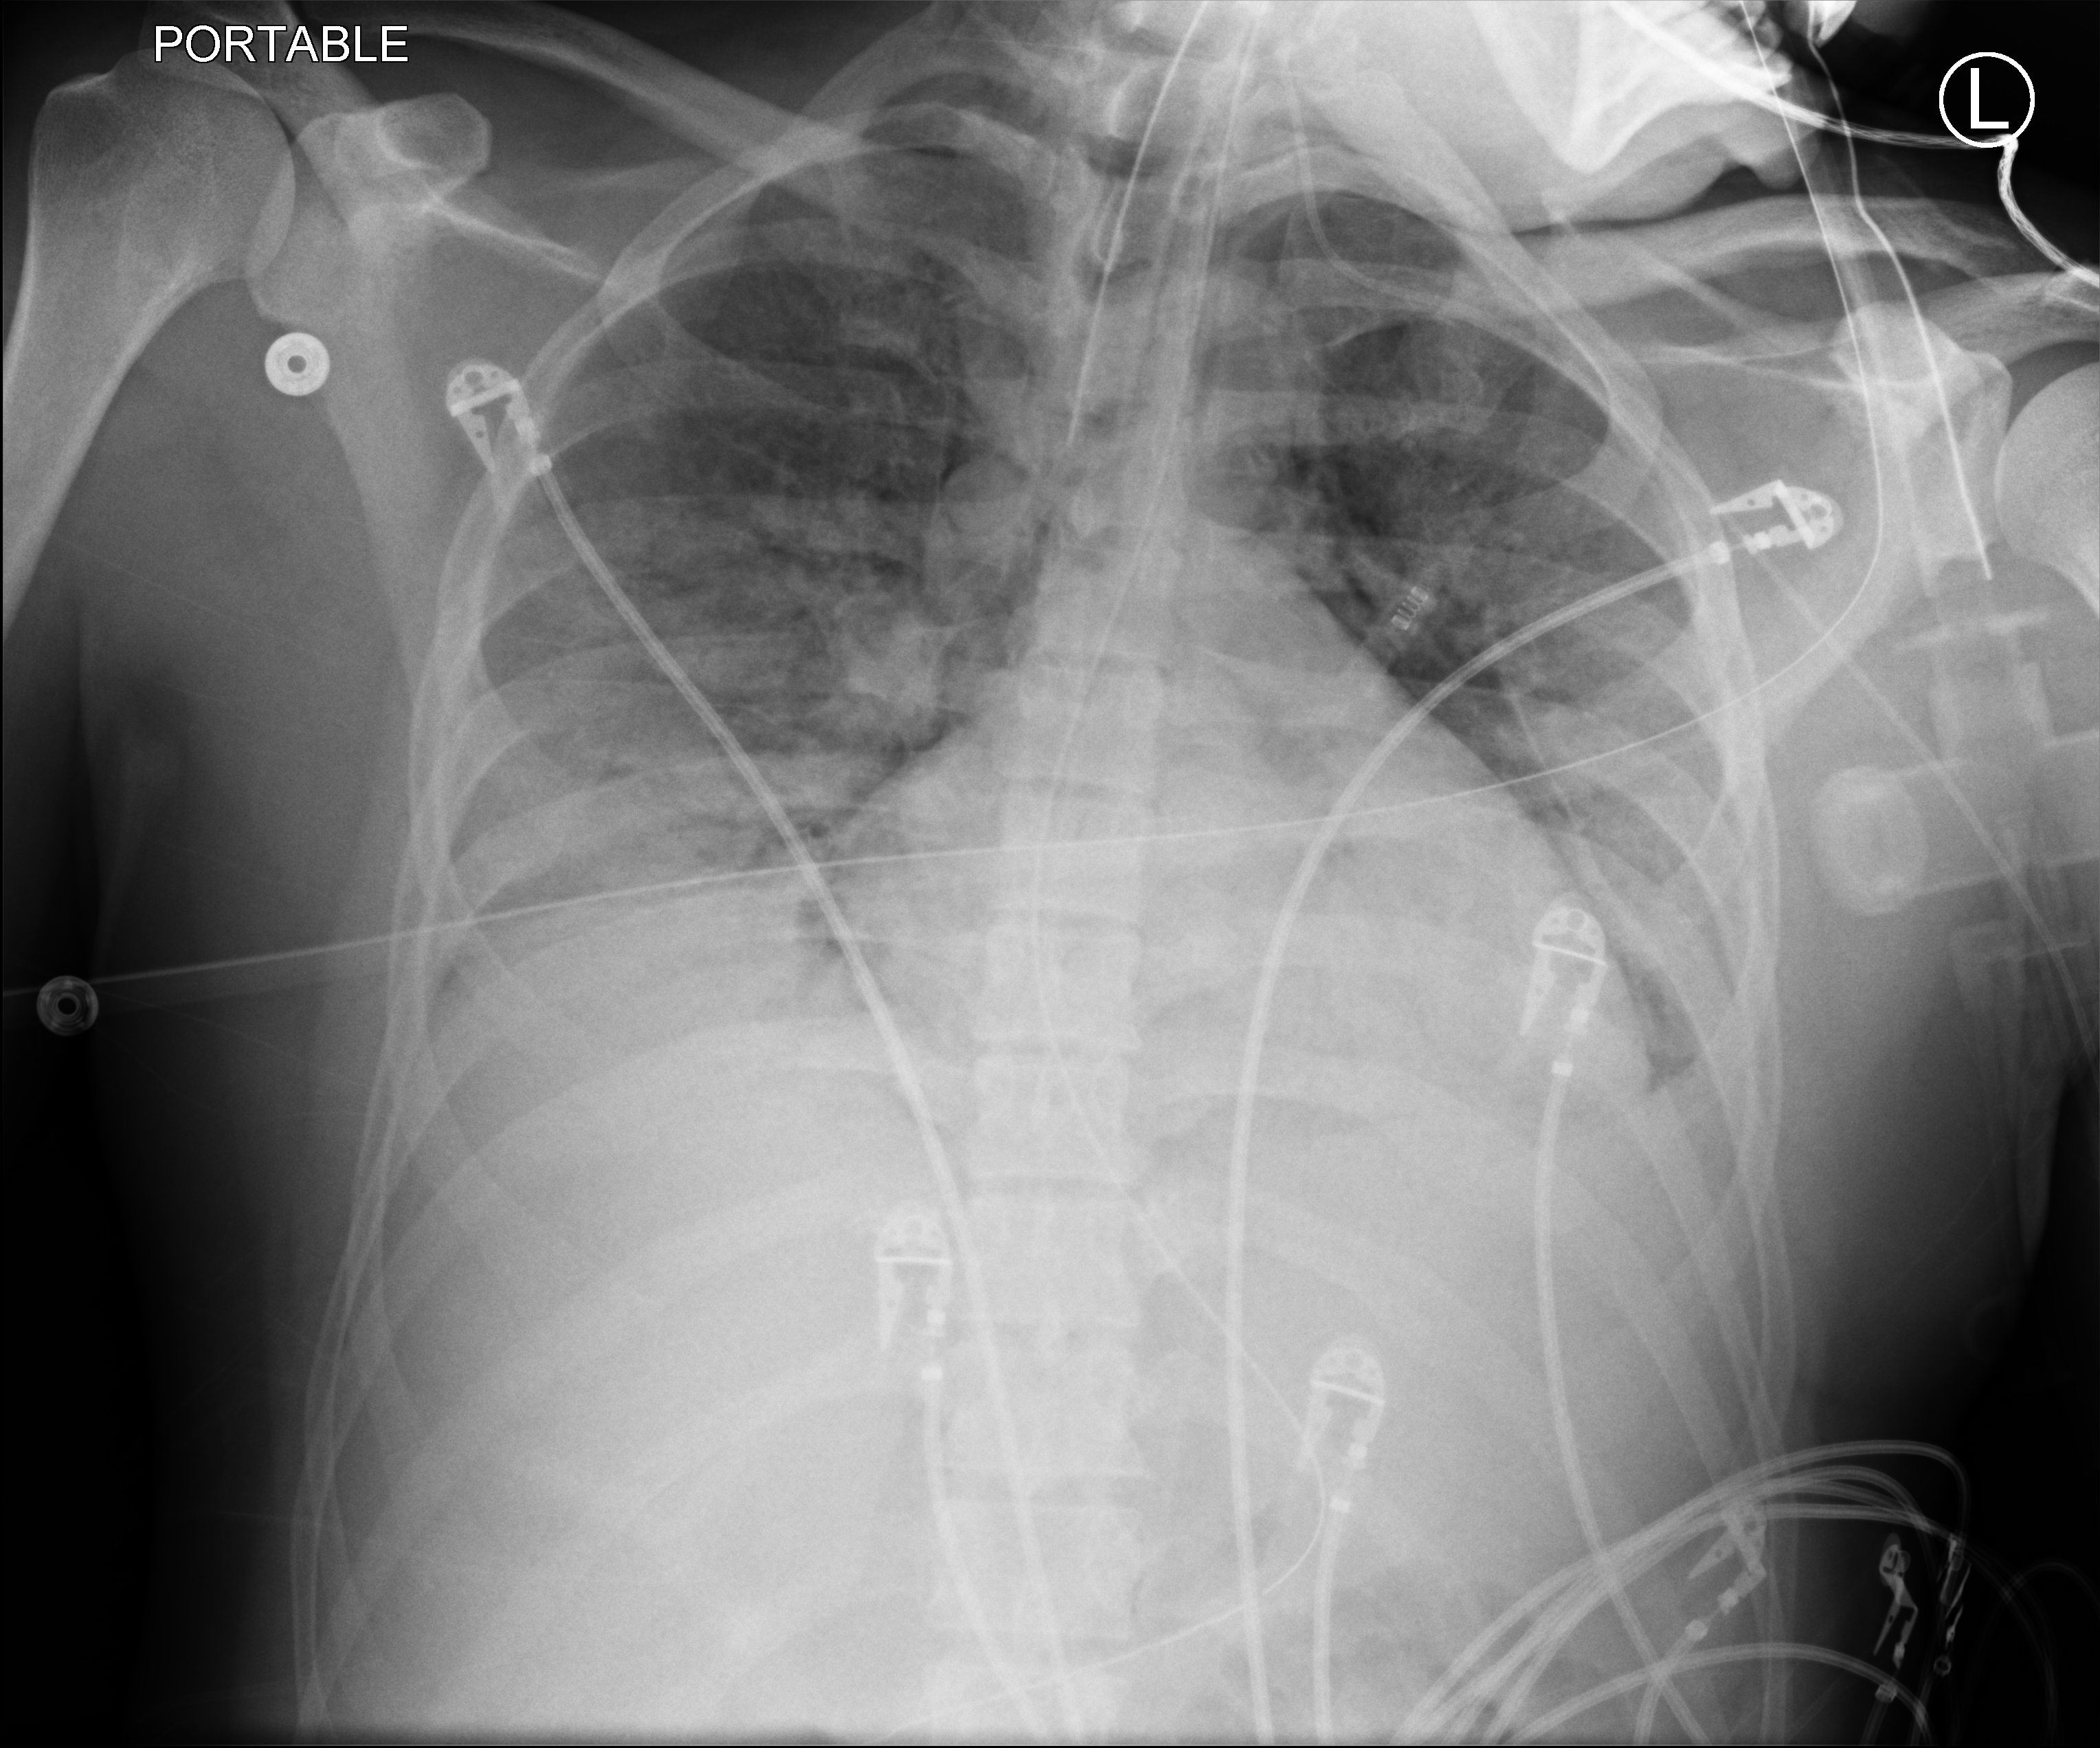
Portable chest radiograph; anteroposterior (AP) projection. Male patient hospitalised with COVID-19, age 18–59 years.
Hospital-stay facts (about this admission, not read from this image; timing relative to this image not recorded): admitted to intensive care during this hospital stay: yes.